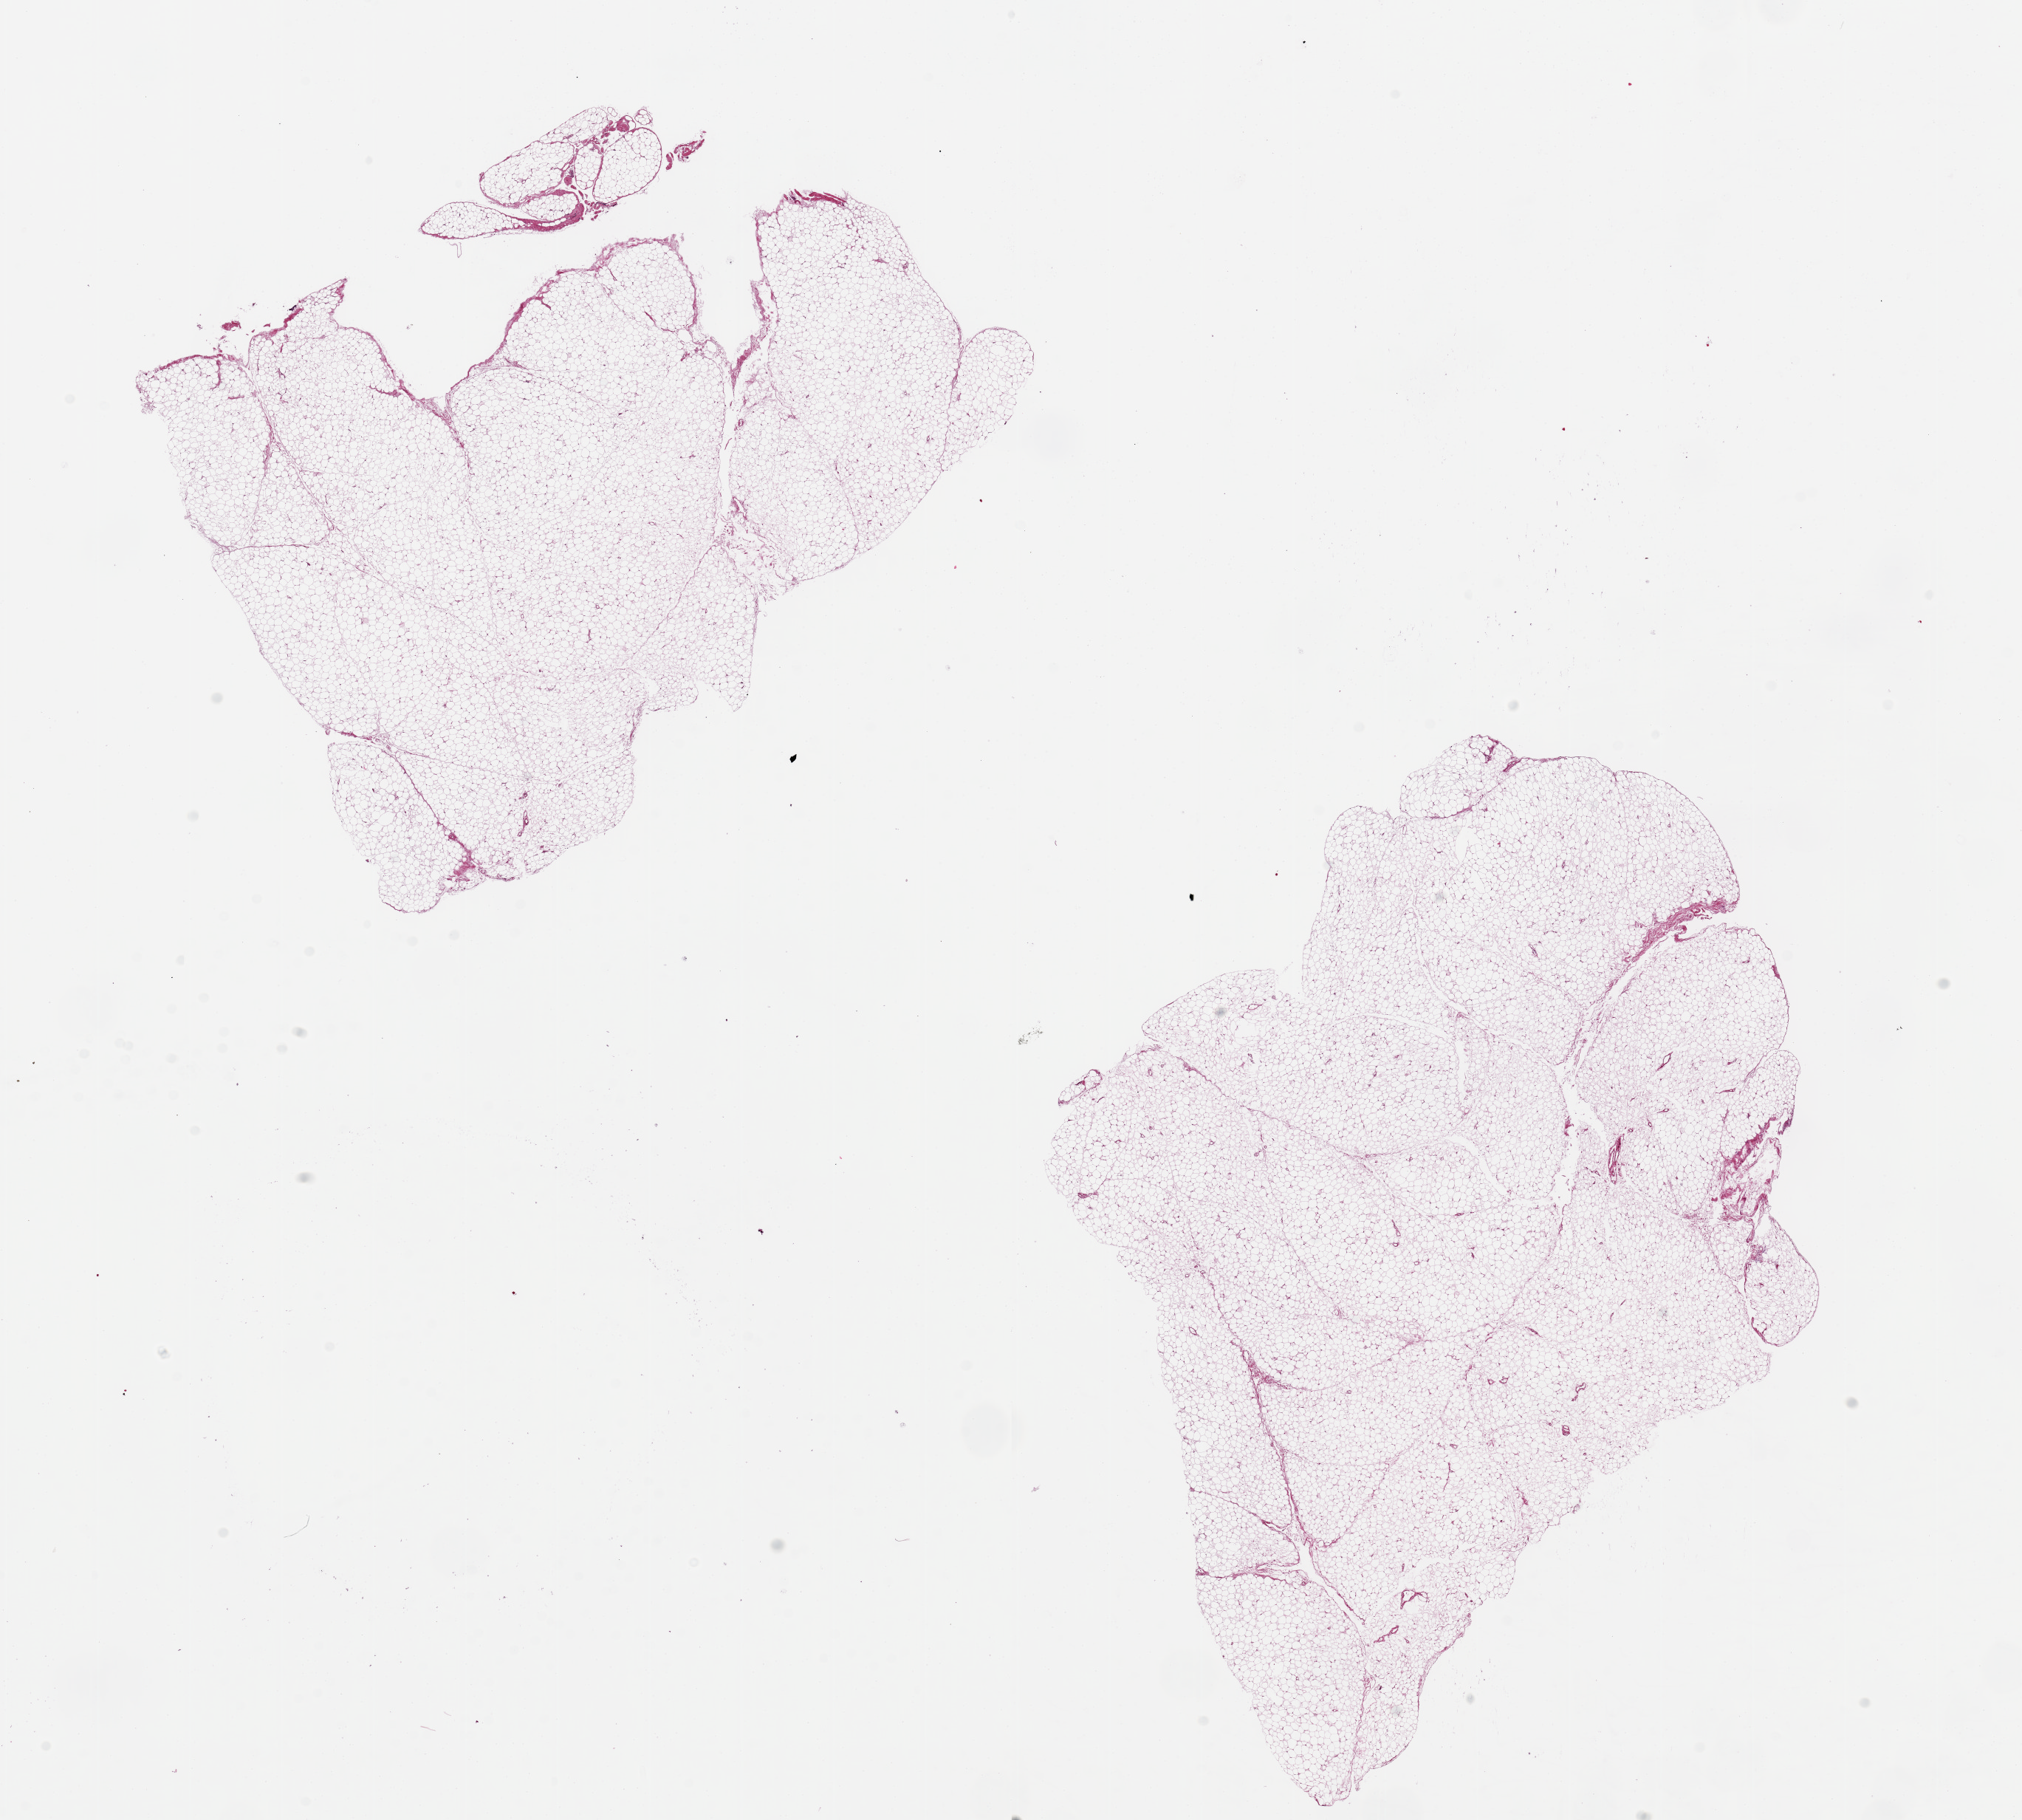
Whole-slide image, H&E stain, shown as a low-resolution overview of the whole scanned area (about 21.7 x 19.5 mm); PAXgene-fixed paraffin-embedded (PFPE) section; section of omentum (target tissue); tissue donor sample. Female donor.
- reviewer comment on this tissue sample: 2 pieces, 9x7 & 9x8mm;. No fixation artifacts